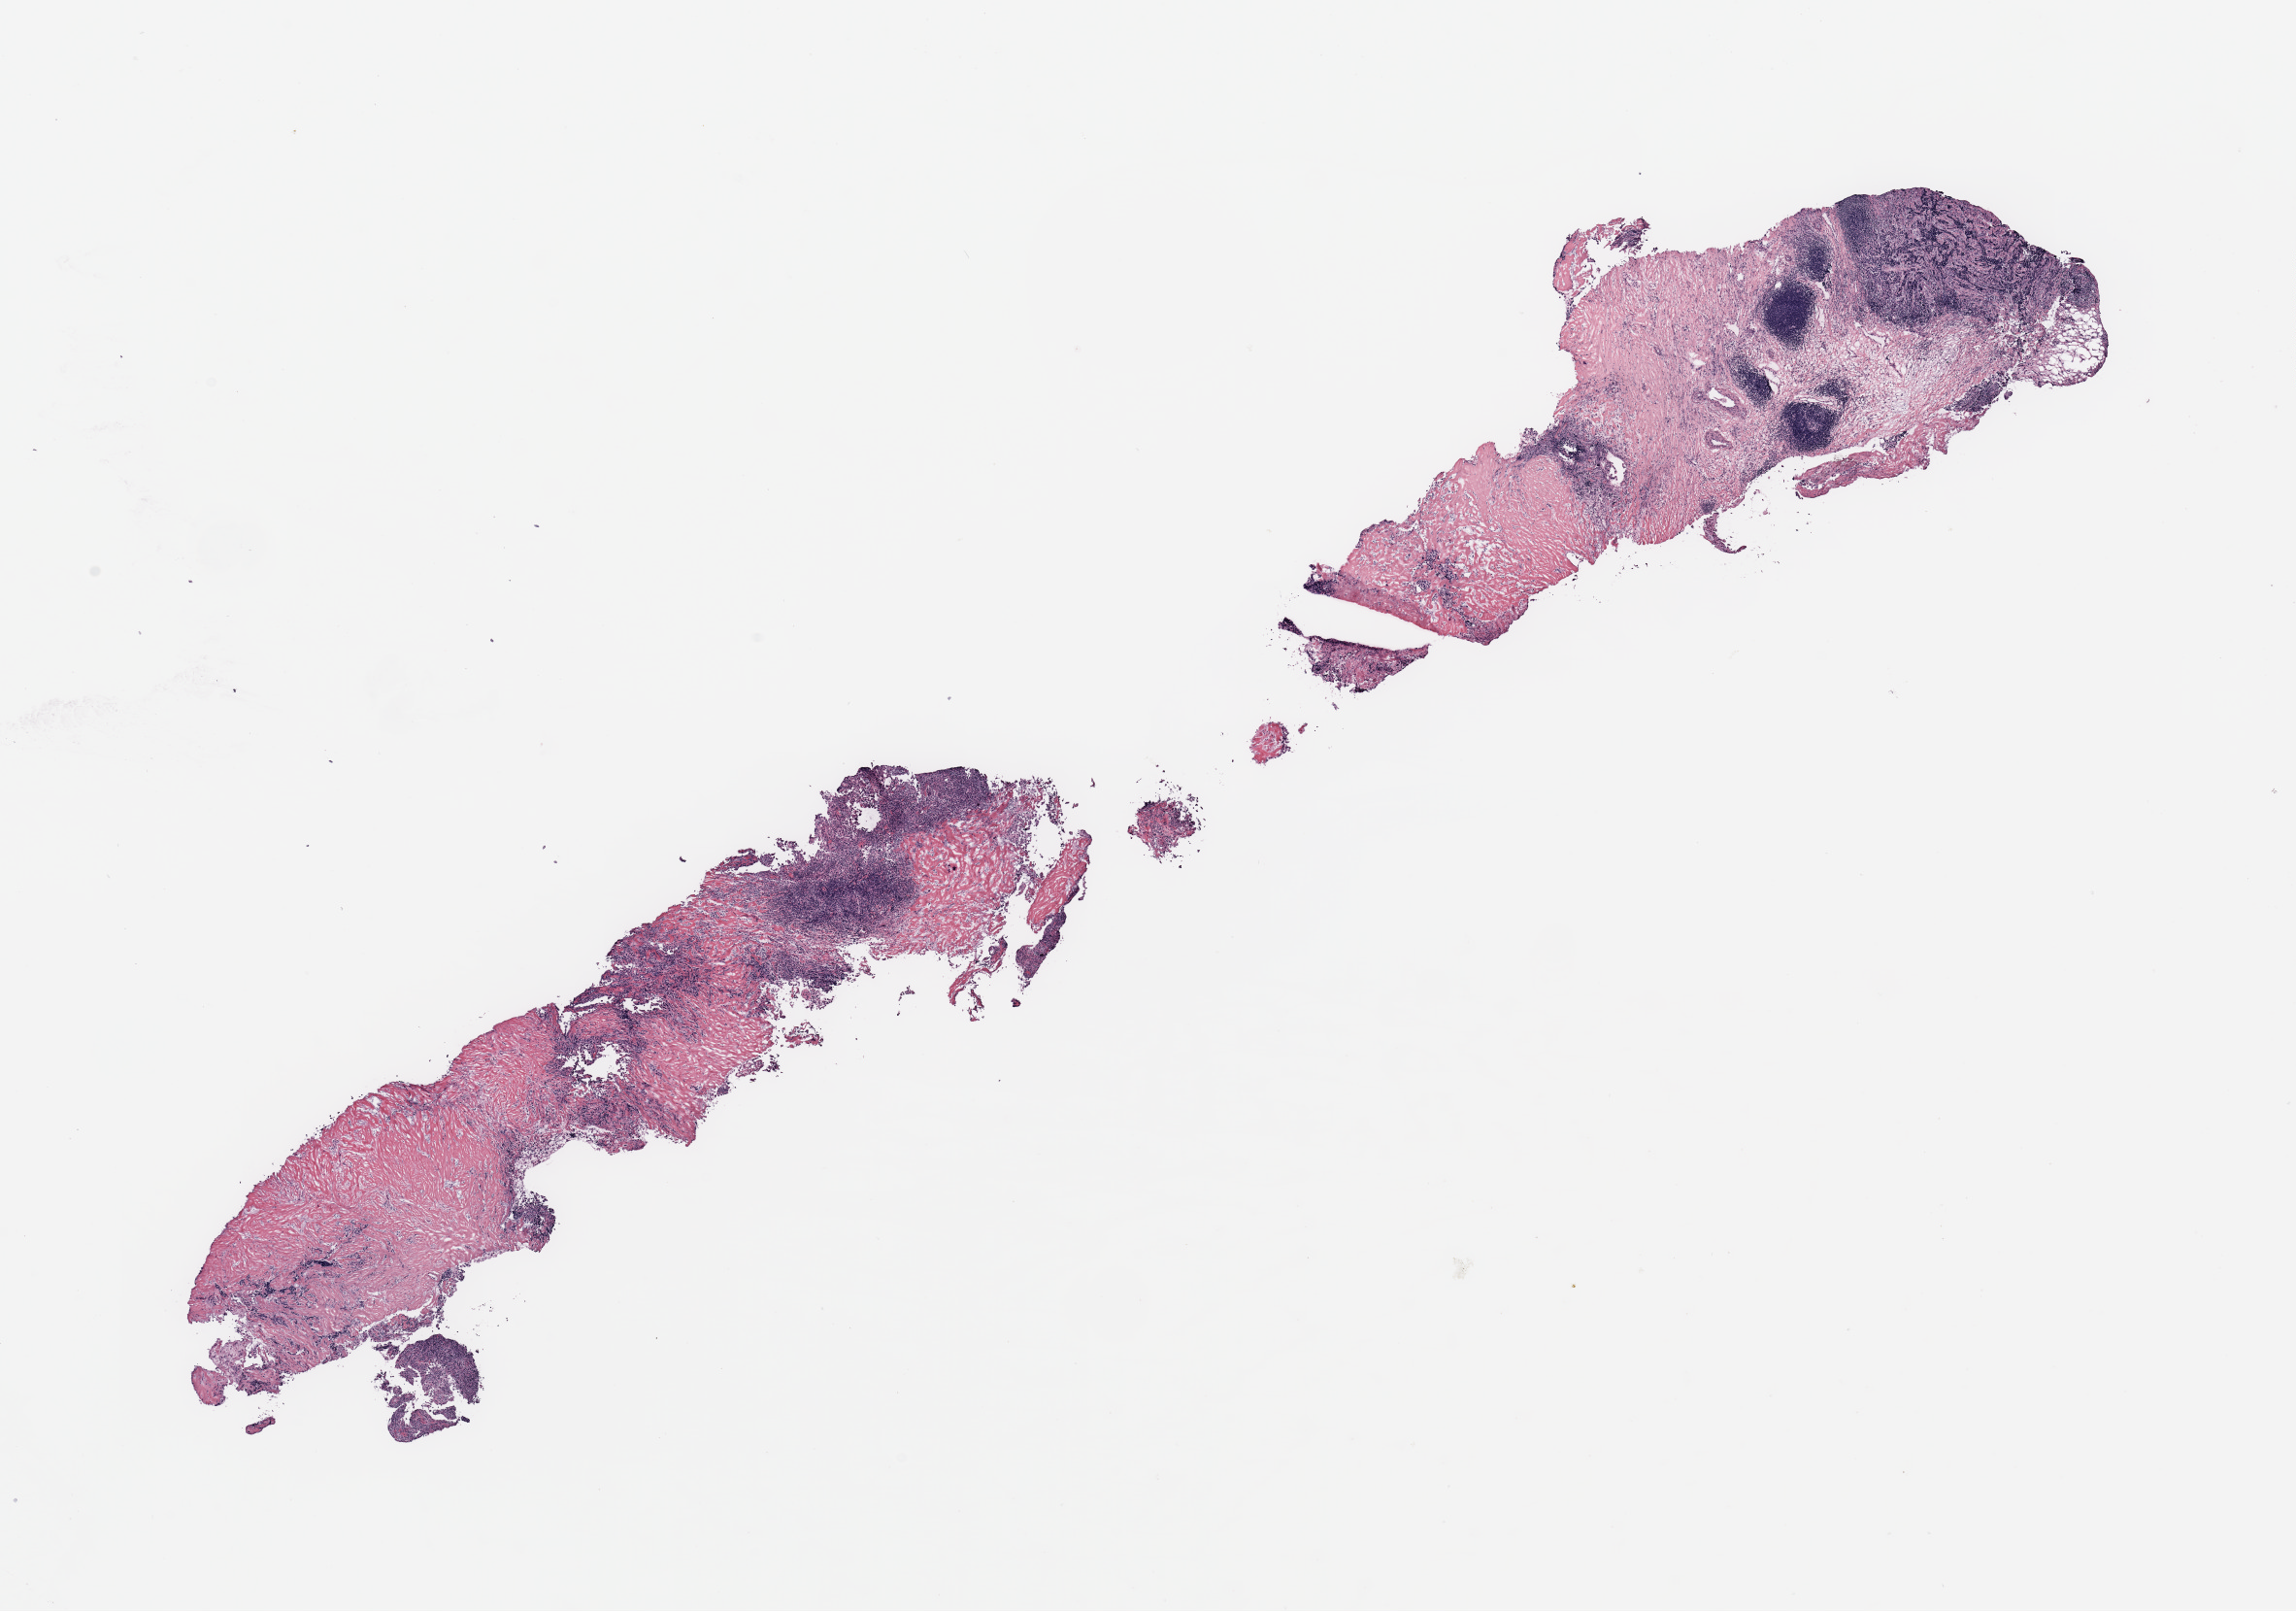
H&E-stained whole-slide image — low-resolution overview of the scanned area, about 18.7 x 13.1 mm; breast, tumour tissue. Female, 84 y/o.
Diagnosis: Infiltrating duct carcinoma, NOS. AJCC pathologic stage: IIIA.